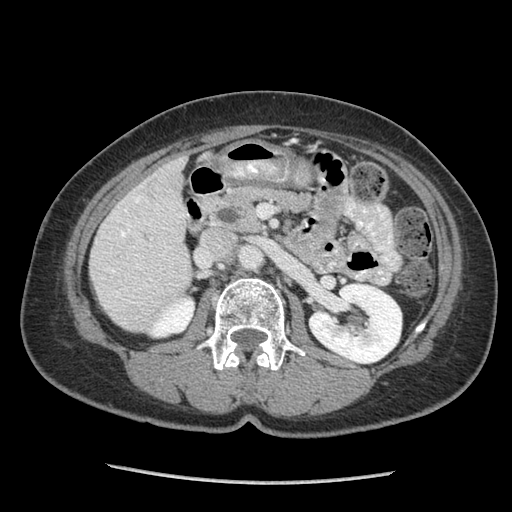
Contrast-enhanced abdominal CT (liver protocol), one axial slice; slice 31 of 105 in the series (ordered by position); reconstruction kernel STANDARD; soft-tissue window (W 400 / L 40 HU); 2.5 mm slice thickness; 512 × 512 image matrix, field of view 340 × 340 mm. Case-level facts recorded for this patient, not image findings: diagnosis: hepatocellular carcinoma (patient treated with transarterial chemoembolisation; whether this scan precedes or follows treatment is not stated here); TNM stage (as recorded): Stage-I; Child-Pugh class: A.
Structures marked on this image (semi-automatic segmentation, software-assisted and operator-edited):
- liver parenchyma outside the tumour (the mass and vessels are separate outlines, so this box may not span the whole liver): bounding box (x1, y1, x2, y2) in pixels: (90, 154, 192, 330)
- liver vessels: (102, 186, 181, 286)